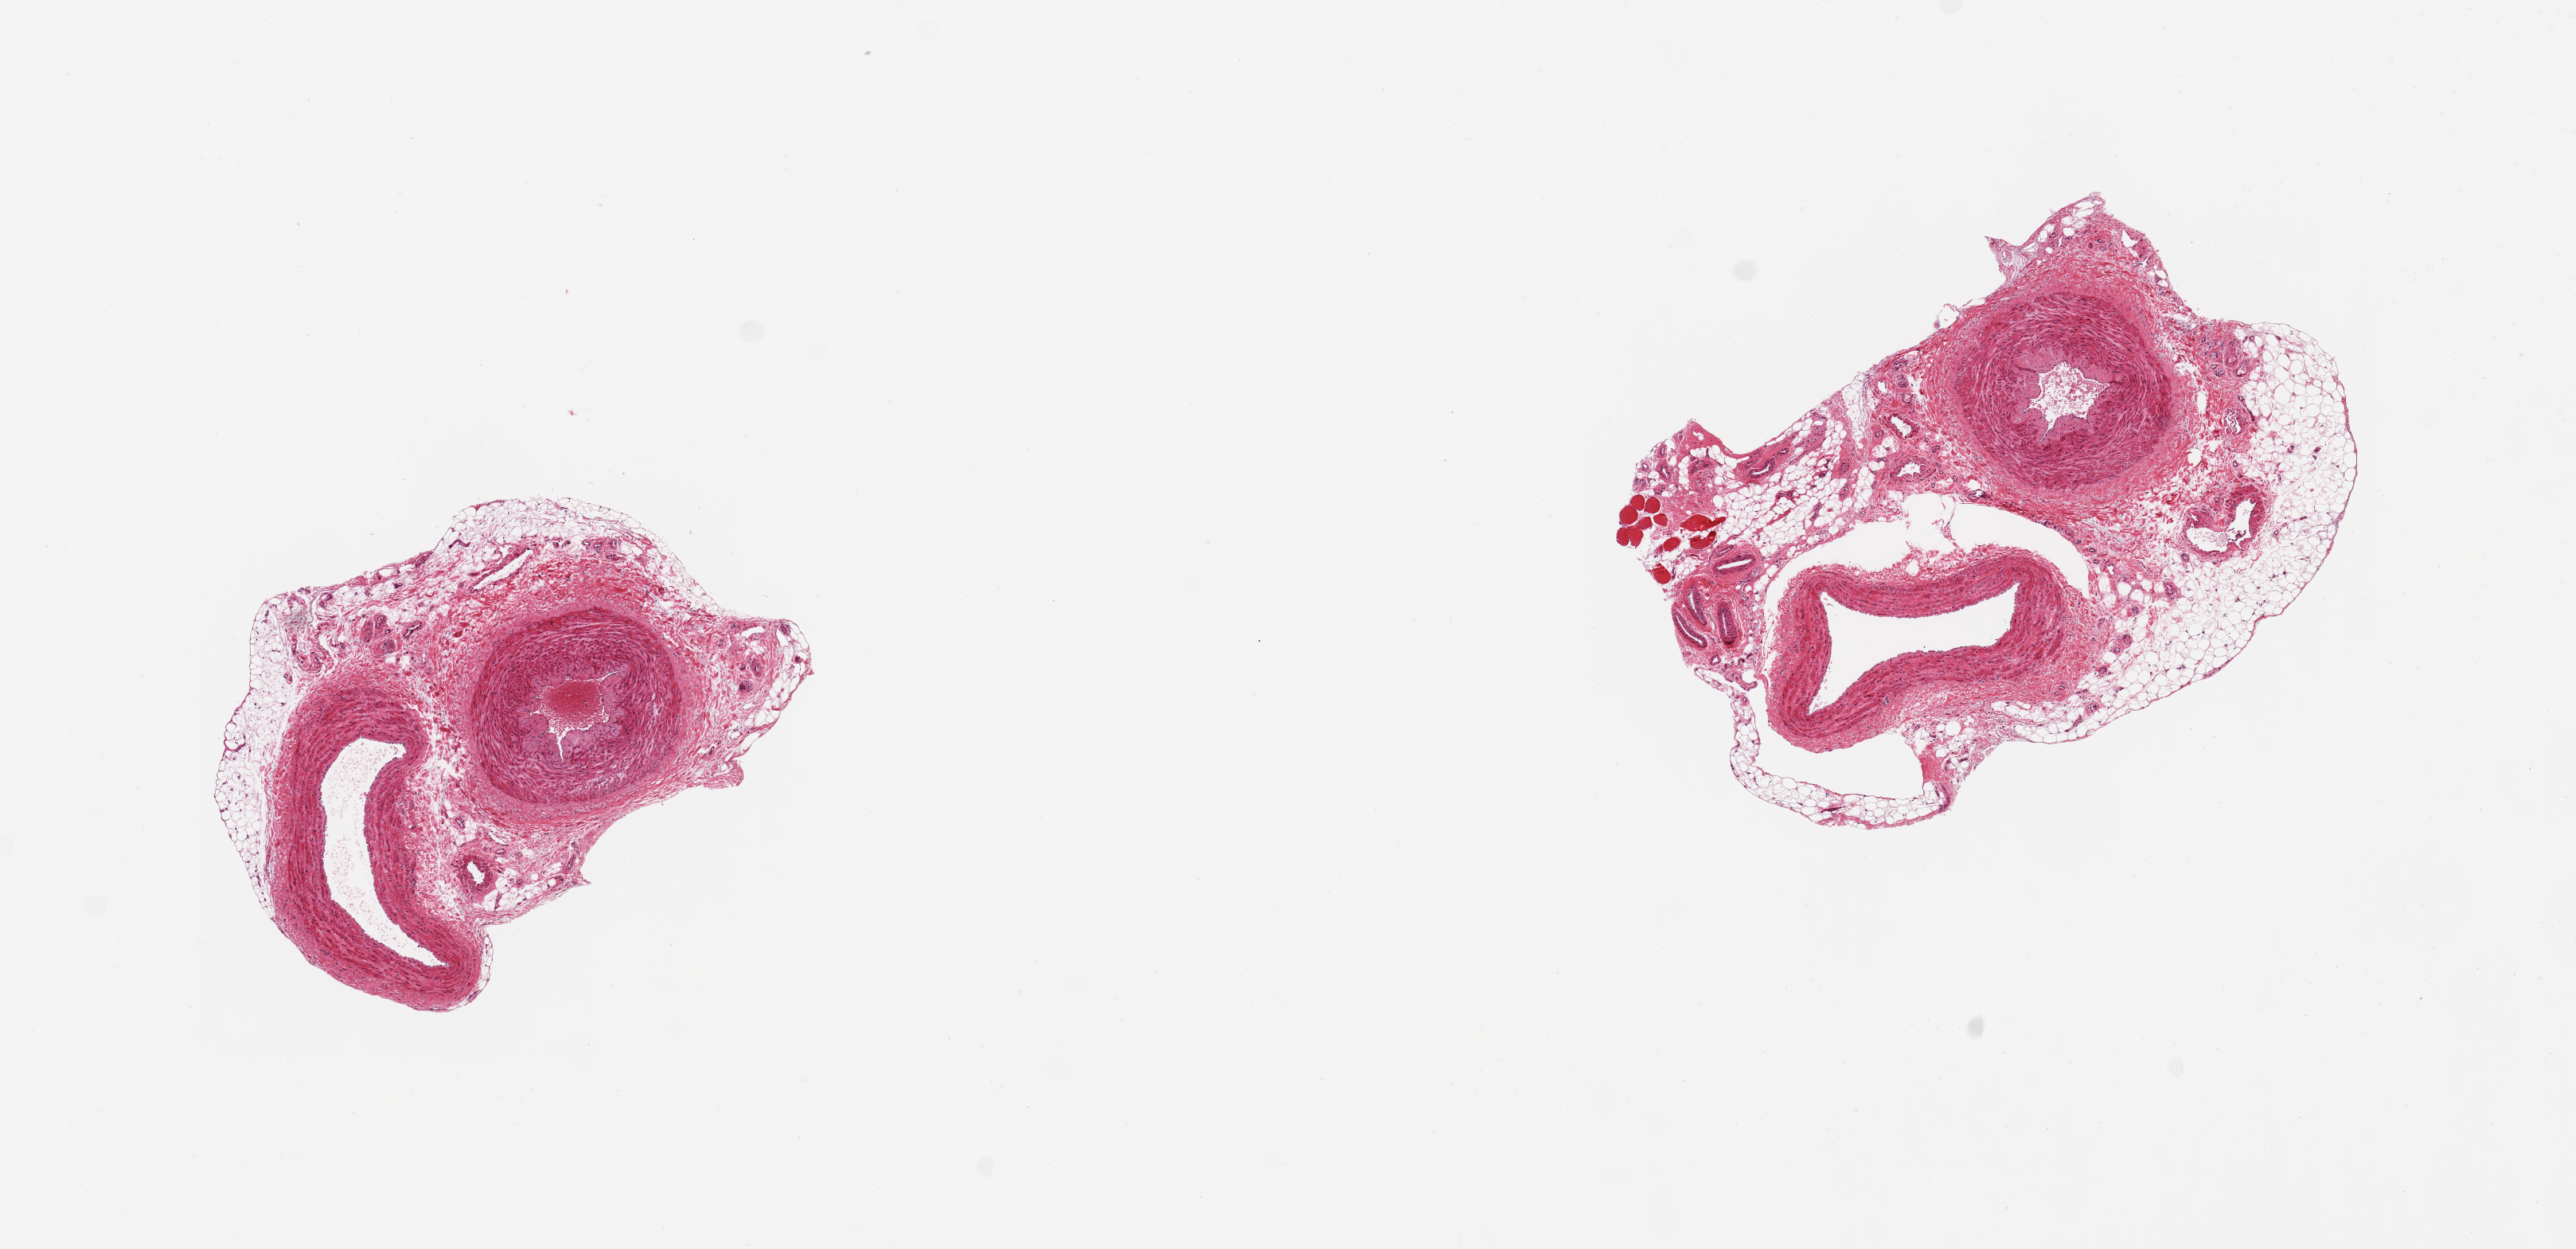
Whole-slide image, haematoxylin and eosin stain, whole scanned area (about 12.8 x 6.2 mm, from a 20x scan) shown as a low-resolution overview, PAXgene-fixed paraffin-embedded (PFPE) section, target tissue: tibial artery, tissue donor sample. Male donor.
Review note (as recorded): 2 pieces, each with 1 1mm artery and 1.5mm vein; 20% adipose tissue.